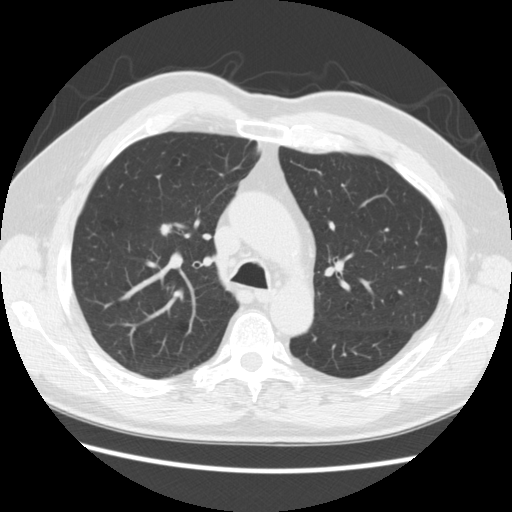
Low-dose screening chest CT, one axial slice; slice 176 of 259 in the series (ordered by position); reconstruction kernel STANDARD; 120 kVp; lung window (W 1500 / L -600 HU); 2.5 mm slice thickness; 512 × 512 image matrix.
Structures marked on this image (outlined manually by an expert reader):
- lesion 1 (tumor, upper lobe of right lung): bounding box [x1, y1, x2, y2] px = [160, 224, 171, 235]